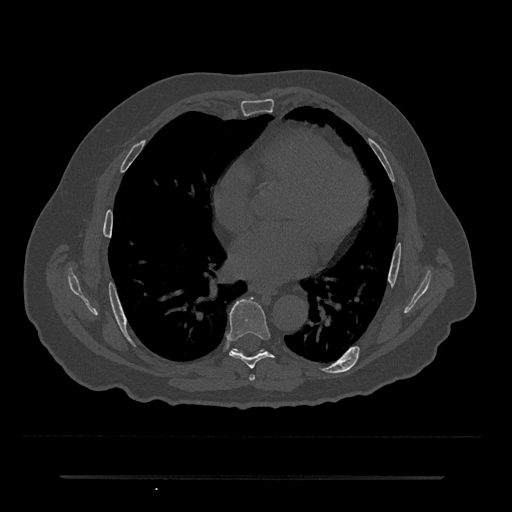
CT including the spine, one axial slice; slice 376 of 797 in the series (ordered by position); reconstruction kernel Br40s/3; 120 kVp; bone window (W 1800 / L 400 HU); 0.5 mm slice thickness; 512 × 512 image matrix. Patient: male, 69 years. From the clinical record (not read from this slice): primary cancer: prostate.
Annotated regions visible in this slice (semi-automatic segmentation, software-assisted and operator-edited):
- T6 vertebra: bounding box <249,375,255,381> (left, top, right, bottom; pixels)
- T7 vertebra: <229,297,274,369>